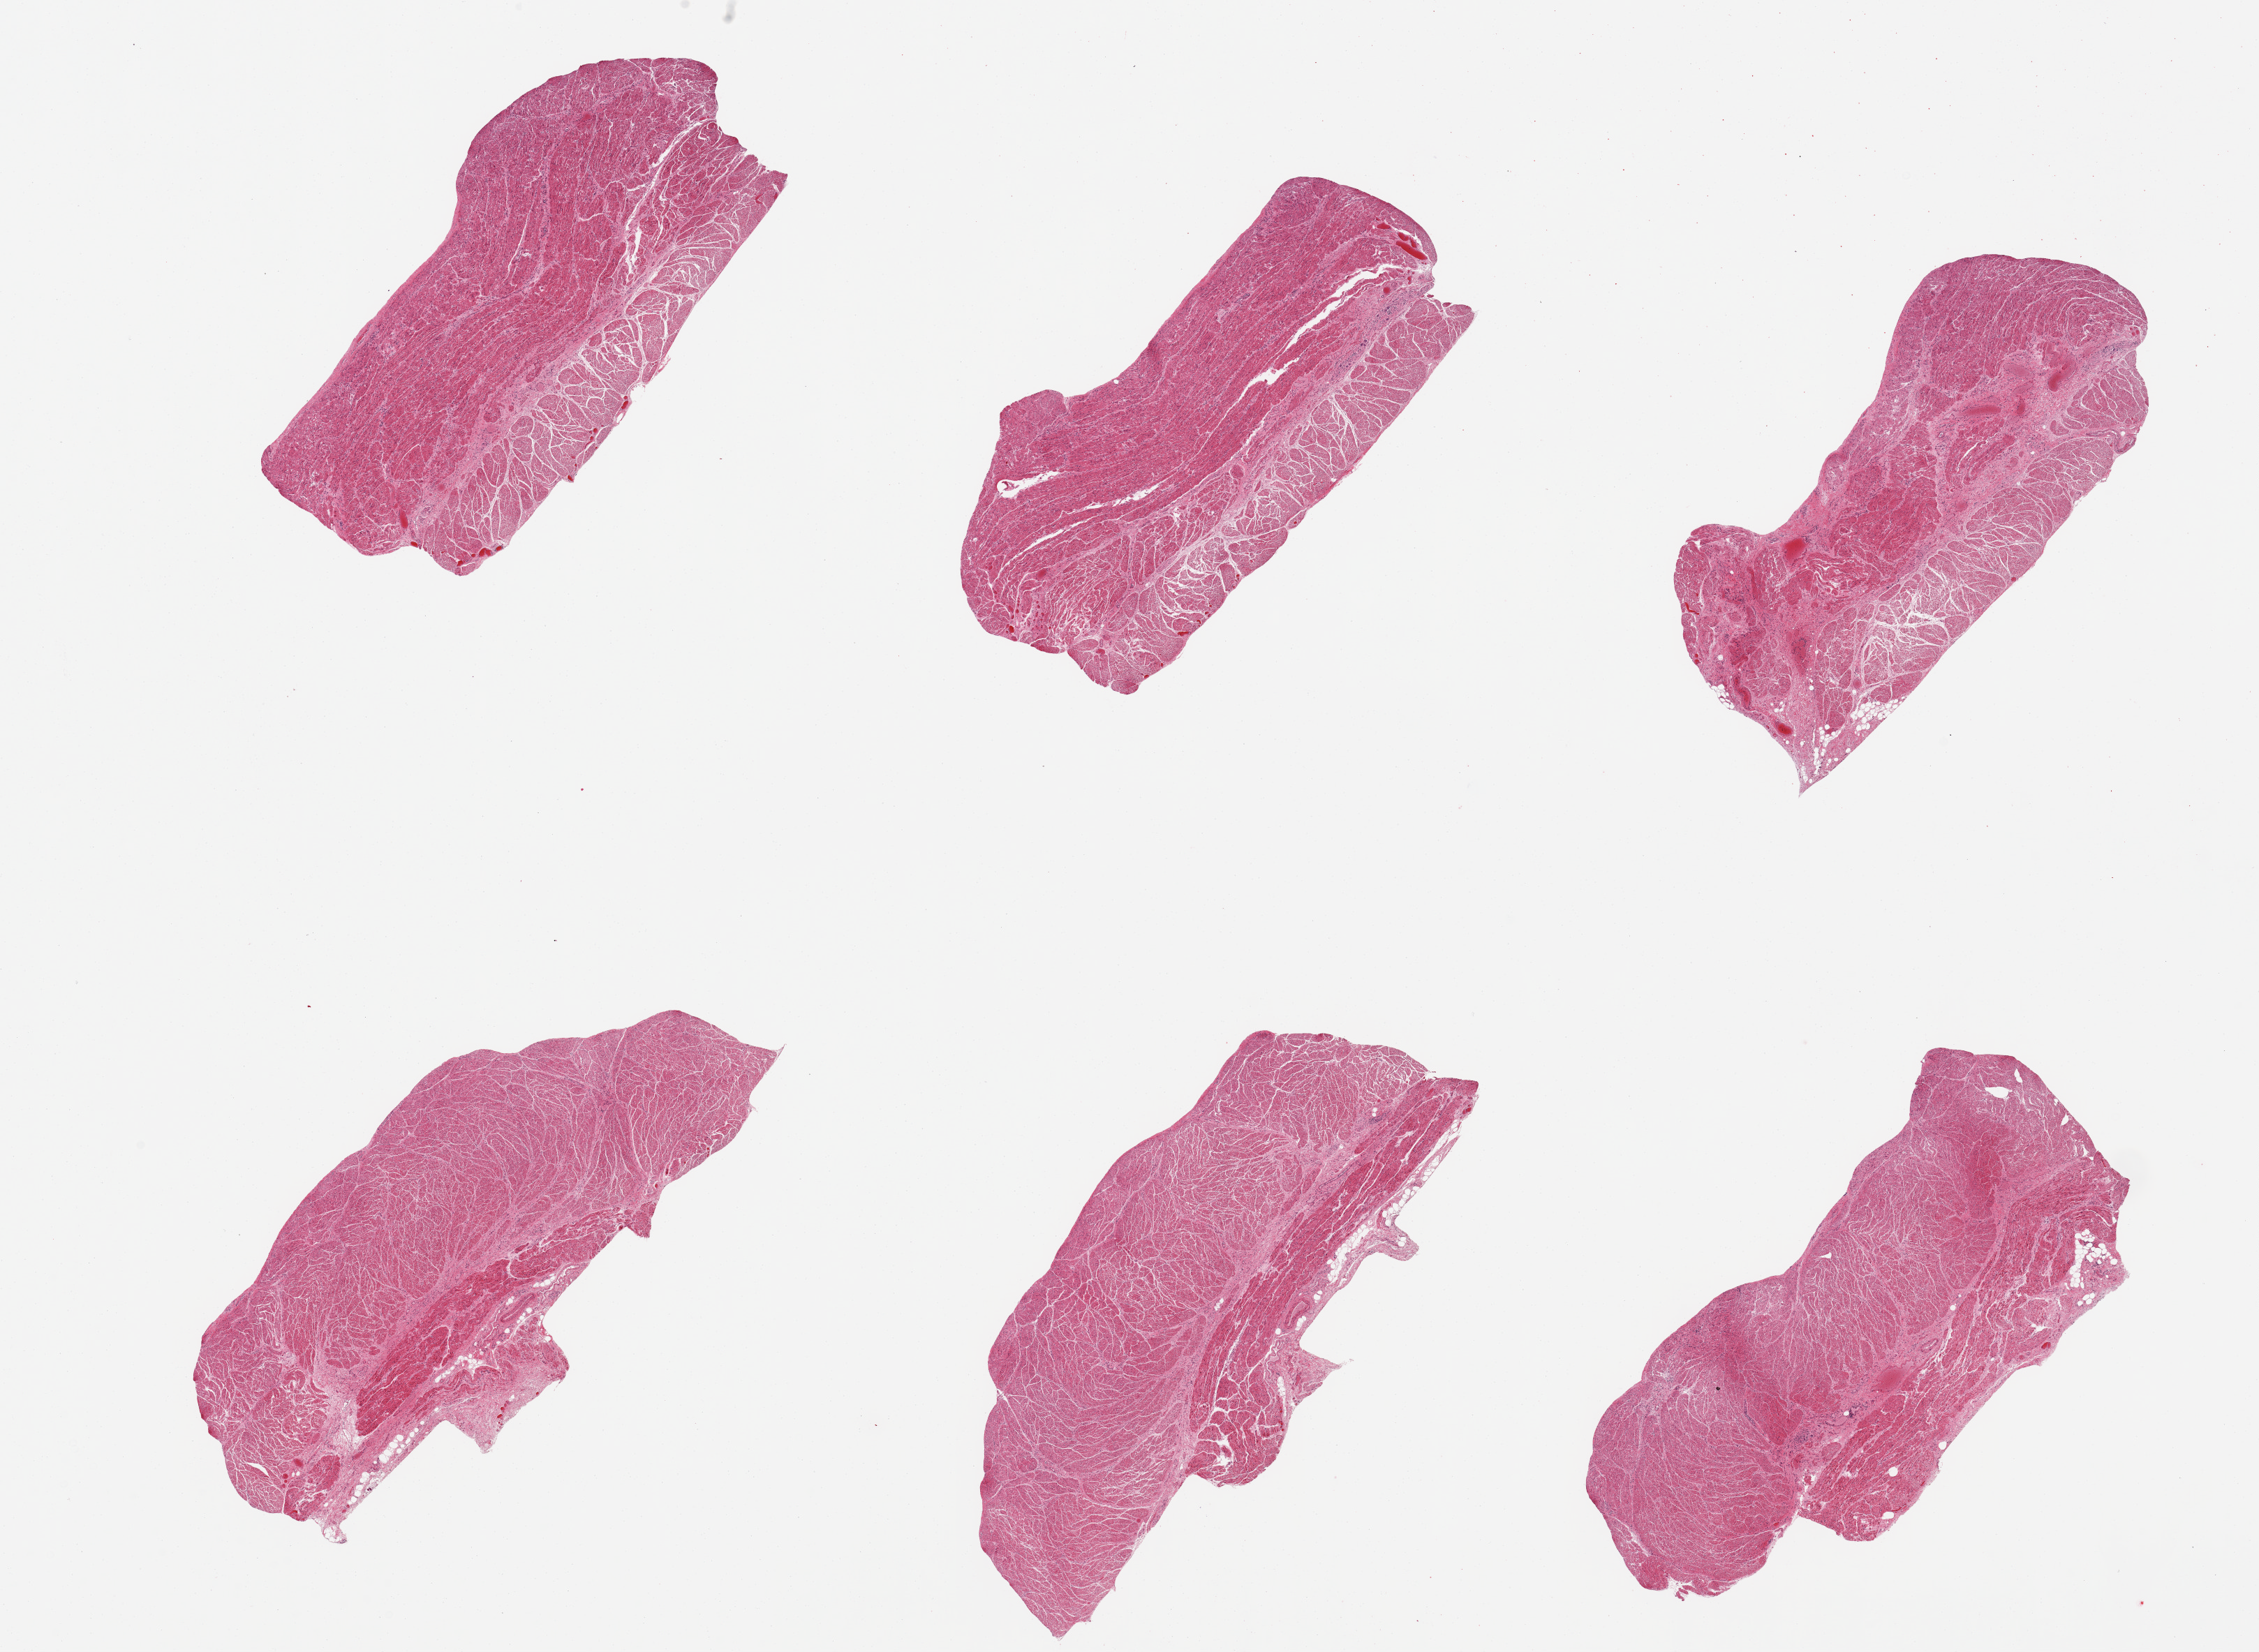
Whole-slide image, haematoxylin and eosin stain — whole scanned area (about 25.6 x 18.7 mm, from a 20x scan) shown as a low-resolution overview; PAXgene-fixed, paraffin-embedded tissue; section of gastroesophageal junction (target tissue); tissue donor sample.
Pathologist's review note for this sample: 6 pieces, confirmed target muscularis.